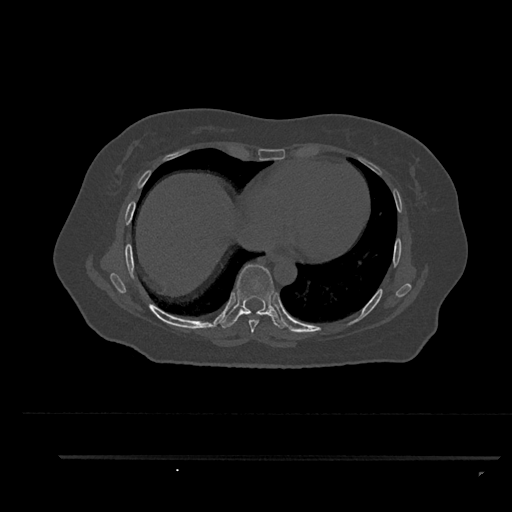
CT including the spine, one axial slice; position 477 of 797 along the scan axis; reconstruction kernel Br40s/3; bone window (W 1800 / L 400 HU); 512 × 512 image matrix, field of view 408 × 408 mm. Female patient, age 44 years. From the clinical record (not read from this slice): primary cancer: renal; vertebrae with lytic lesions (as recorded): L1.
Outlined on this slice (semi-automatic segmentation, software-assisted and operator-edited):
- T7 vertebra: bounding box <248,319,259,333> (left, top, right, bottom; pixels)
- T8 vertebra: <221,264,287,329>